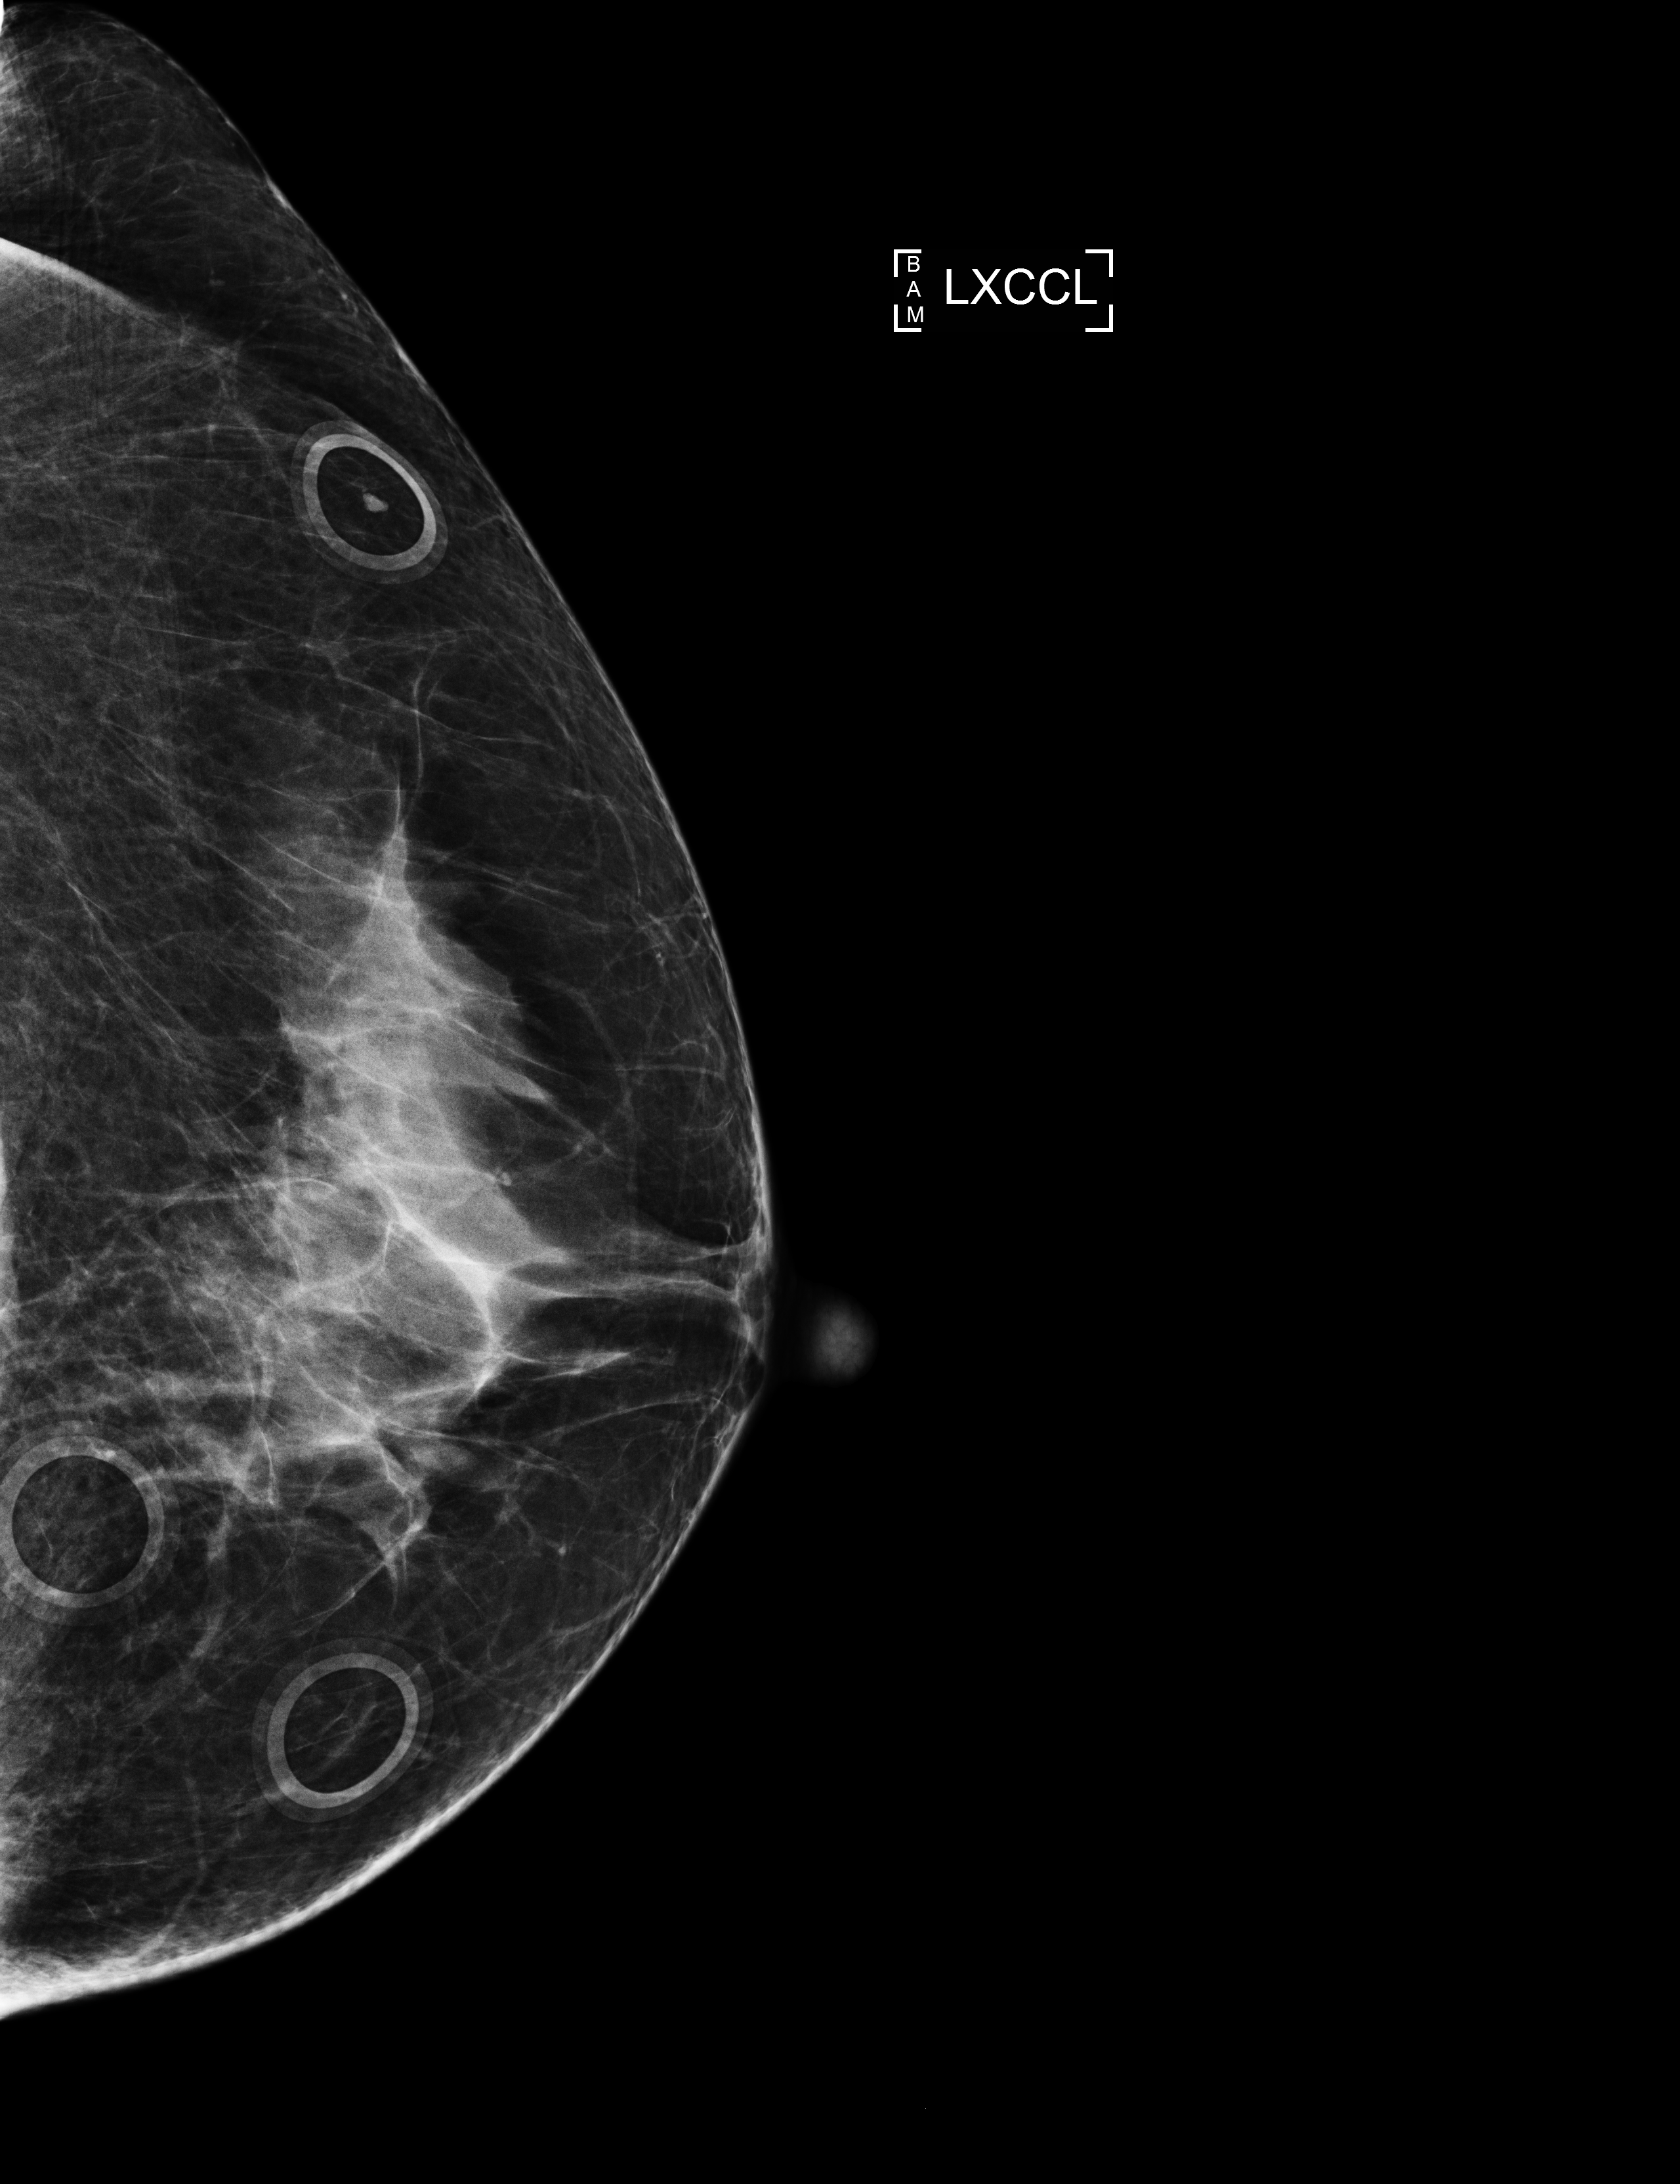
Annual screening mammography examination; compressed breast thickness 67 mm; system: Selenia Dimensions. Patient: female, 60 years.
Image type: full-field digital mammogram. Breast: left. Projection: laterally exaggerated craniocaudal (XCCL) view.